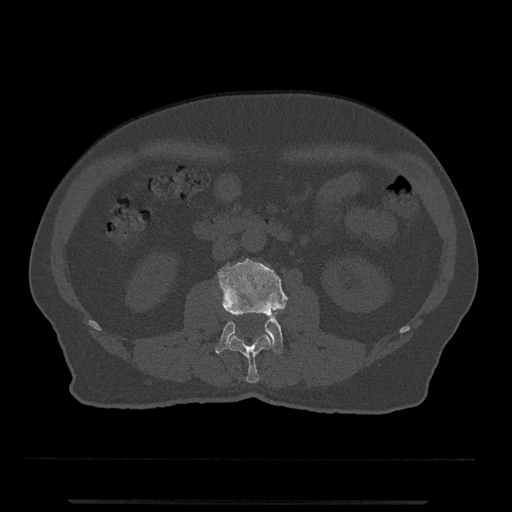
CT including the spine, one axial slice. Position 231 of 797 along the scan axis. Reconstruction kernel Br40s/3. 120 kVp. Bone window (W 1800 / L 400 HU). 512 × 512 image matrix. Male patient, age 63 years. From the clinical record (not read from this slice): primary cancer: prostate.
Outlined on this slice (semi-automatically segmented with operator editing):
- L2 vertebra: bounding box (x1, y1, x2, y2) in pixels: (226, 333, 272, 383)
- L3 vertebra: (215, 258, 288, 354)